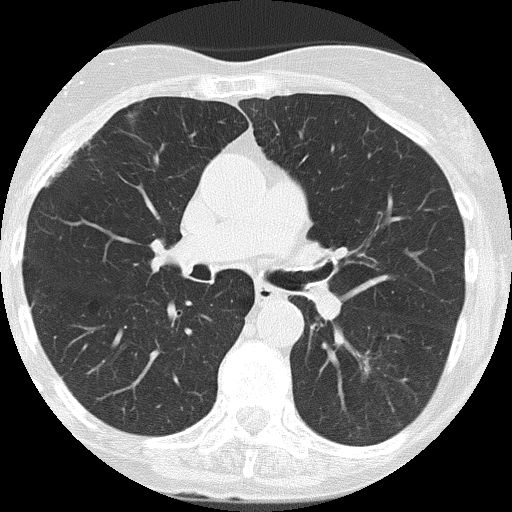
Chest CT (low-dose screening protocol), one axial image. Second annual screen. Lung window (W 1500 / L -600 HU). 2 mm slice thickness. Lung (sharp) reconstruction kernel (FC51). Slice 69 of 159 in the series. Female, age 68 years at enrolment. Former smoker at enrolment.
Lesion marked by an expert reader, box from (x=337, y=341) to (x=395, y=392) px. No non-calcified nodule or mass ≥4 mm was recorded by the screening reader at this exam.